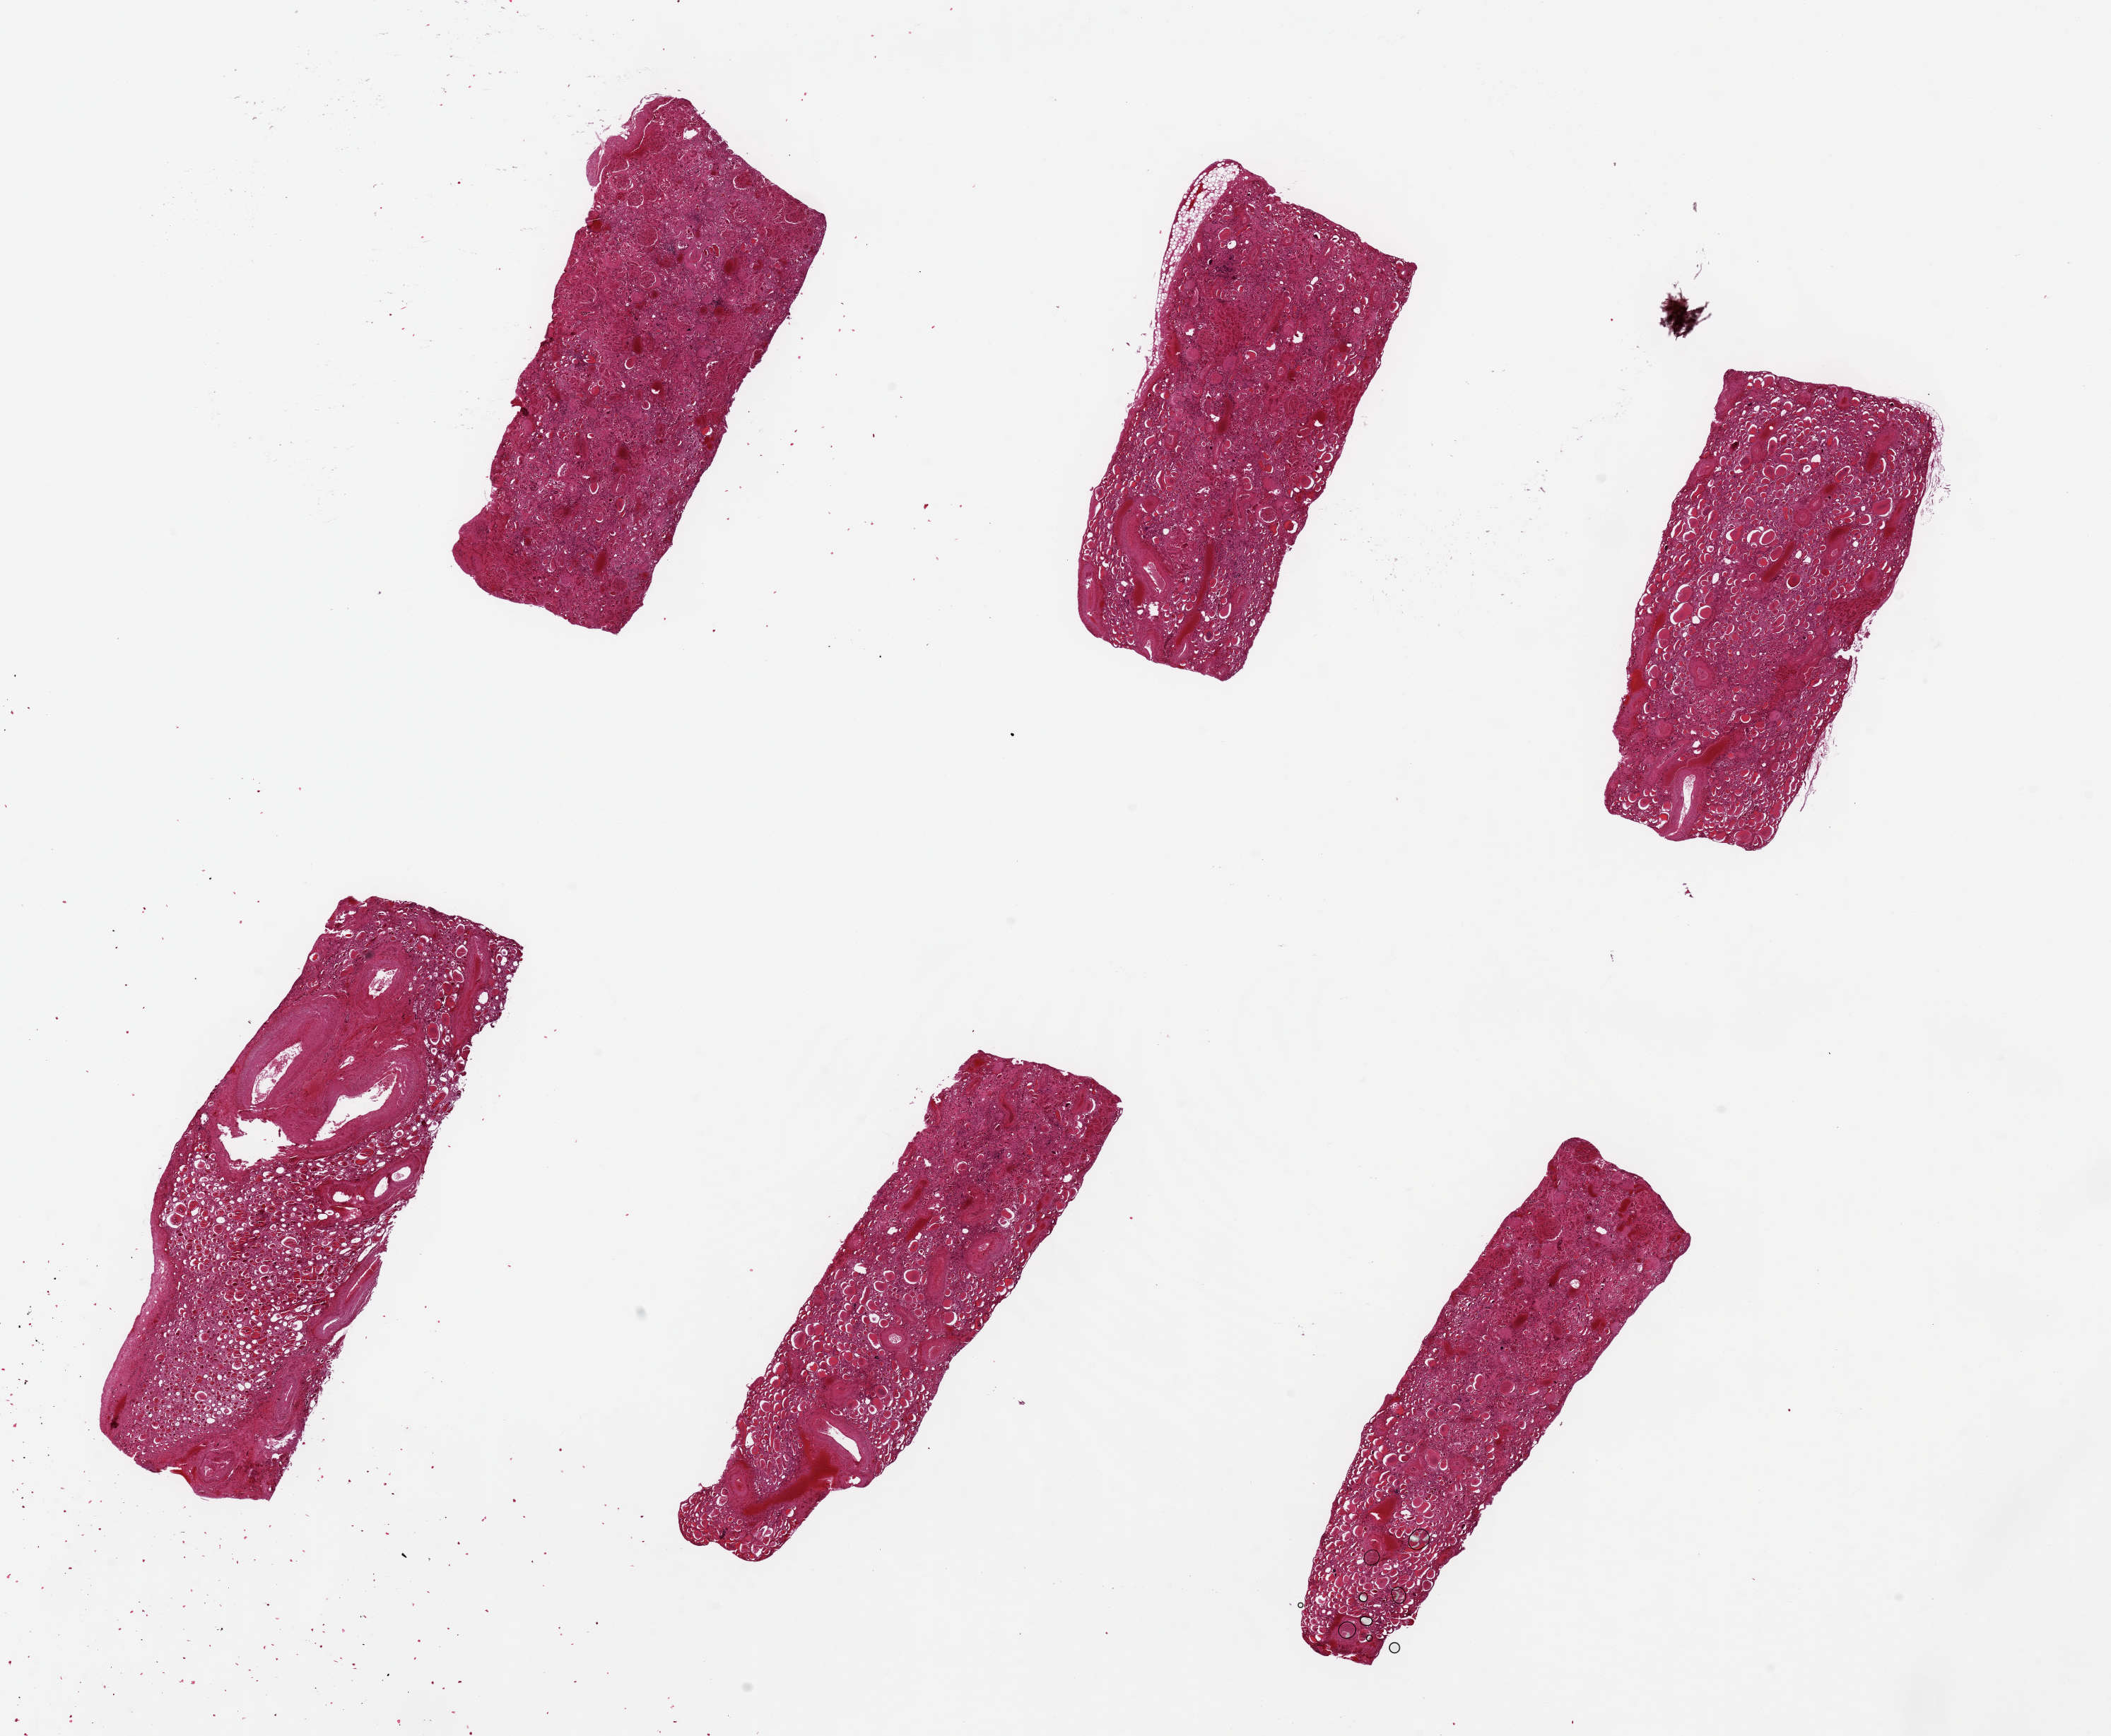
Whole-slide image, H&E stain, shown as a low-resolution overview of the whole scanned area (about 23.6 x 19.4 mm); PAXgene-fixed paraffin-embedded (PFPE) section; target tissue: renal cortex; tissue donor sample. Donor sex: male.
Pathologist's review note for this sample: 6 pieces, Diffuse end-stage fibrosing glomerulonephritis, diffuse thyroidization is evident.